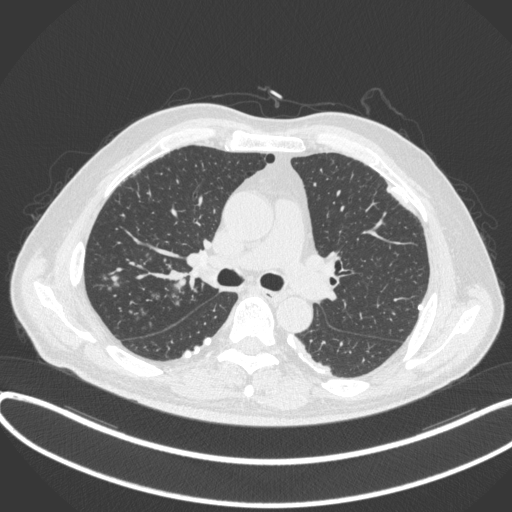
Chest CT, one axial slice; slice 260 of 455 in the series (ordered by position); reconstruction kernel B31f; 120 kVp; lung window (W 1500 / L -600 HU); 512 × 512 image matrix, field of view 400 × 400 mm. Male patient, age 58 years. Case-level facts recorded for this patient, not image findings: clinical TNM (as recorded): T1c N0 M0.
Structures marked on this image (bounding box drawn by a radiologist):
- lung tumour (recorded histology: squamous cell carcinoma): box from (x=166, y=264) to (x=193, y=300) px